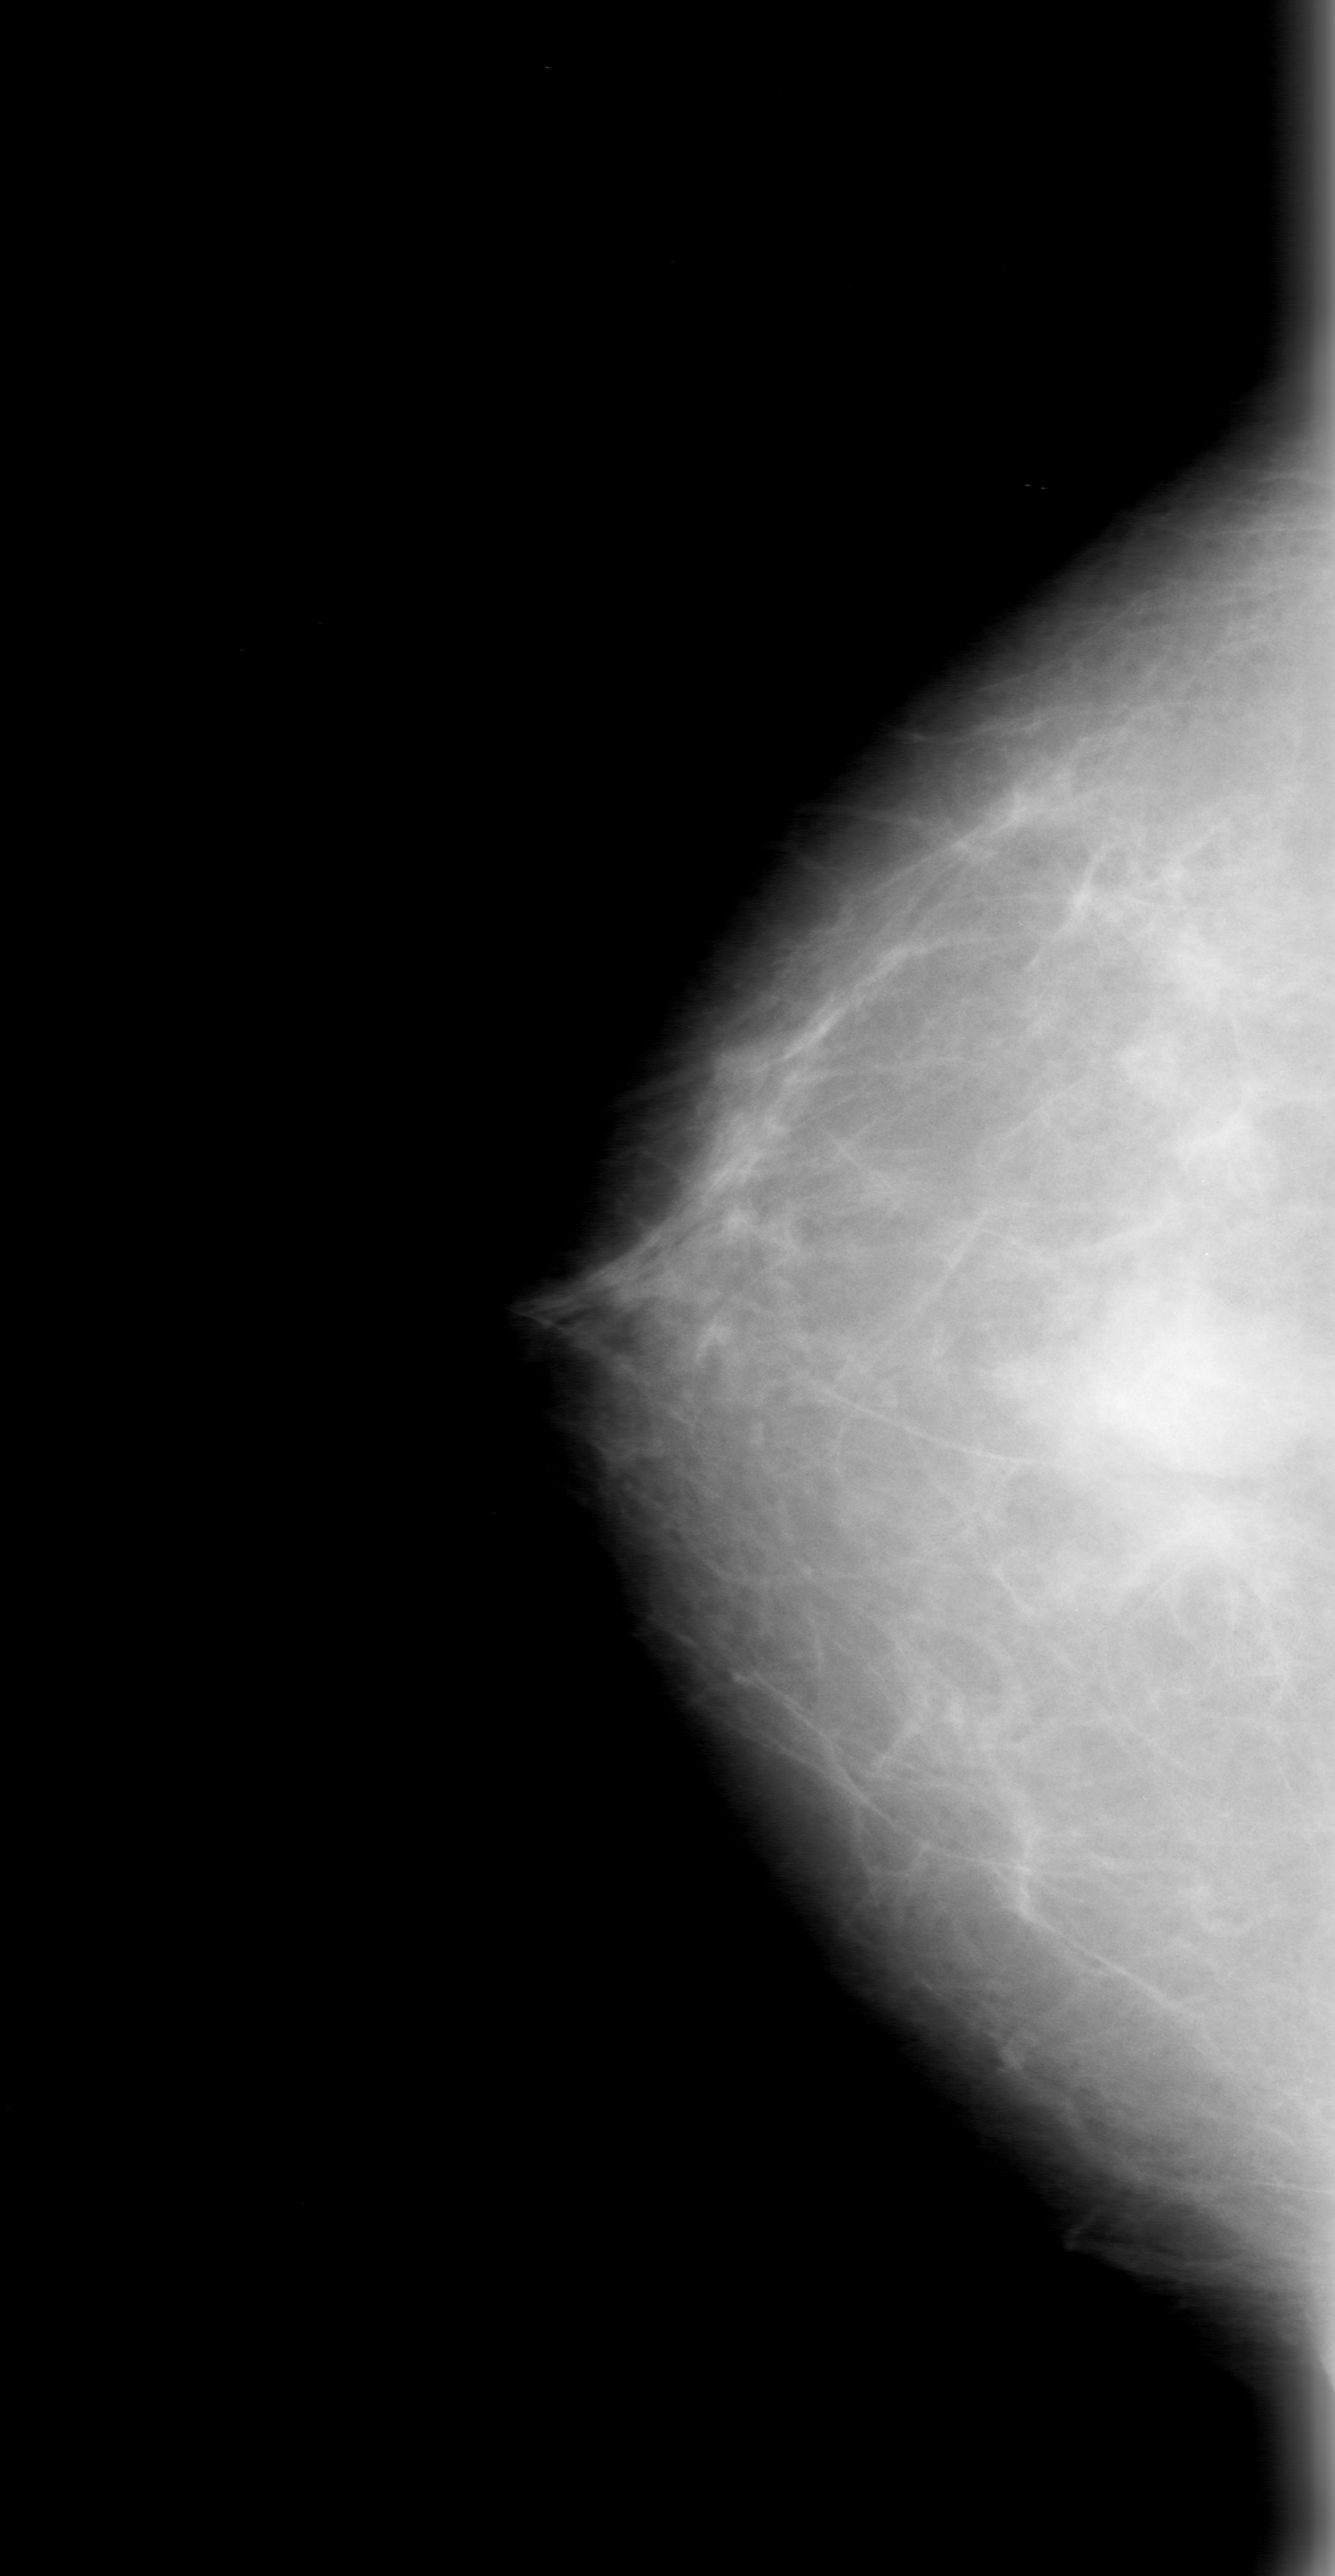
Mammogram (digitized film); right breast; craniocaudal (CC) view; breast composition: almost entirely fatty (BI-RADS density category 1 of 4).
- Radiologist-marked abnormalities on this image: mass, shape oval, margins obscured; BI-RADS assessment category 0; subtlety rating 4 on a 1 (subtle) to 5 (obvious) scale; pathology result (as recorded, not read from the image): benign.